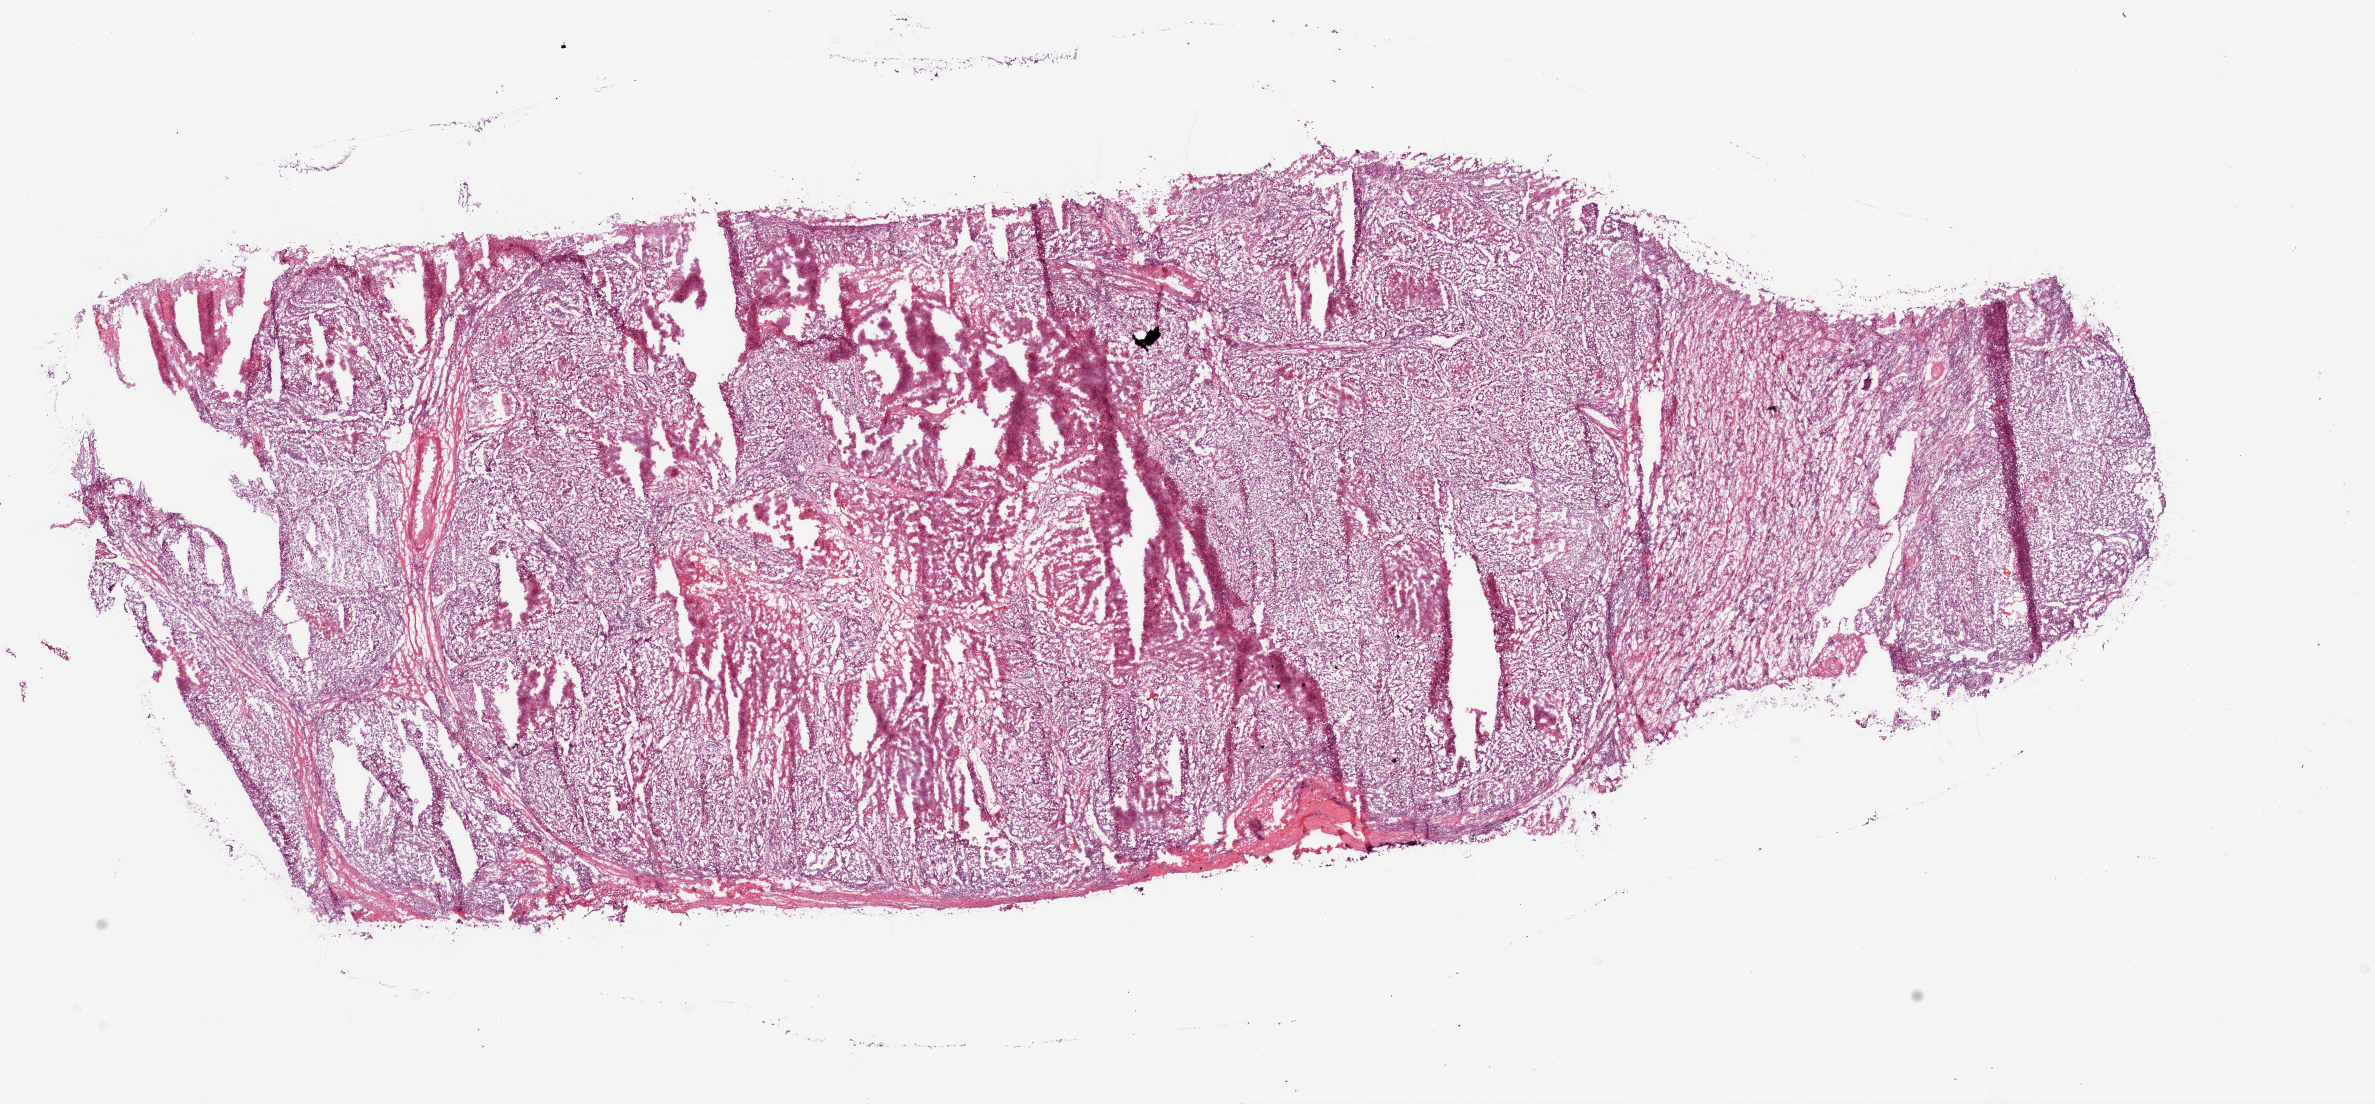
Whole-slide histology image, Hematoxylin and eosin (H&E) stained, whole scanned area (about 19.1 x 8.9 mm) shown as a low-resolution overview; frozen section; kidney, primary tumour sample. Male patient; age at initial diagnosis 69 years. Histologic grade: G4 (undifferentiated). Composition of this section per pathologist review: tumour cells 70%, tumour nuclei 80%, normal cells 0%, stromal cells 10%, necrosis 20%.
Histologic diagnosis: Clear cell adenocarcinoma, NOS. TNM: T3b N1 M0. Laterality: left. AJCC pathologic stage: III. Lymph nodes positive (case pathology): 1 of 1 examined.